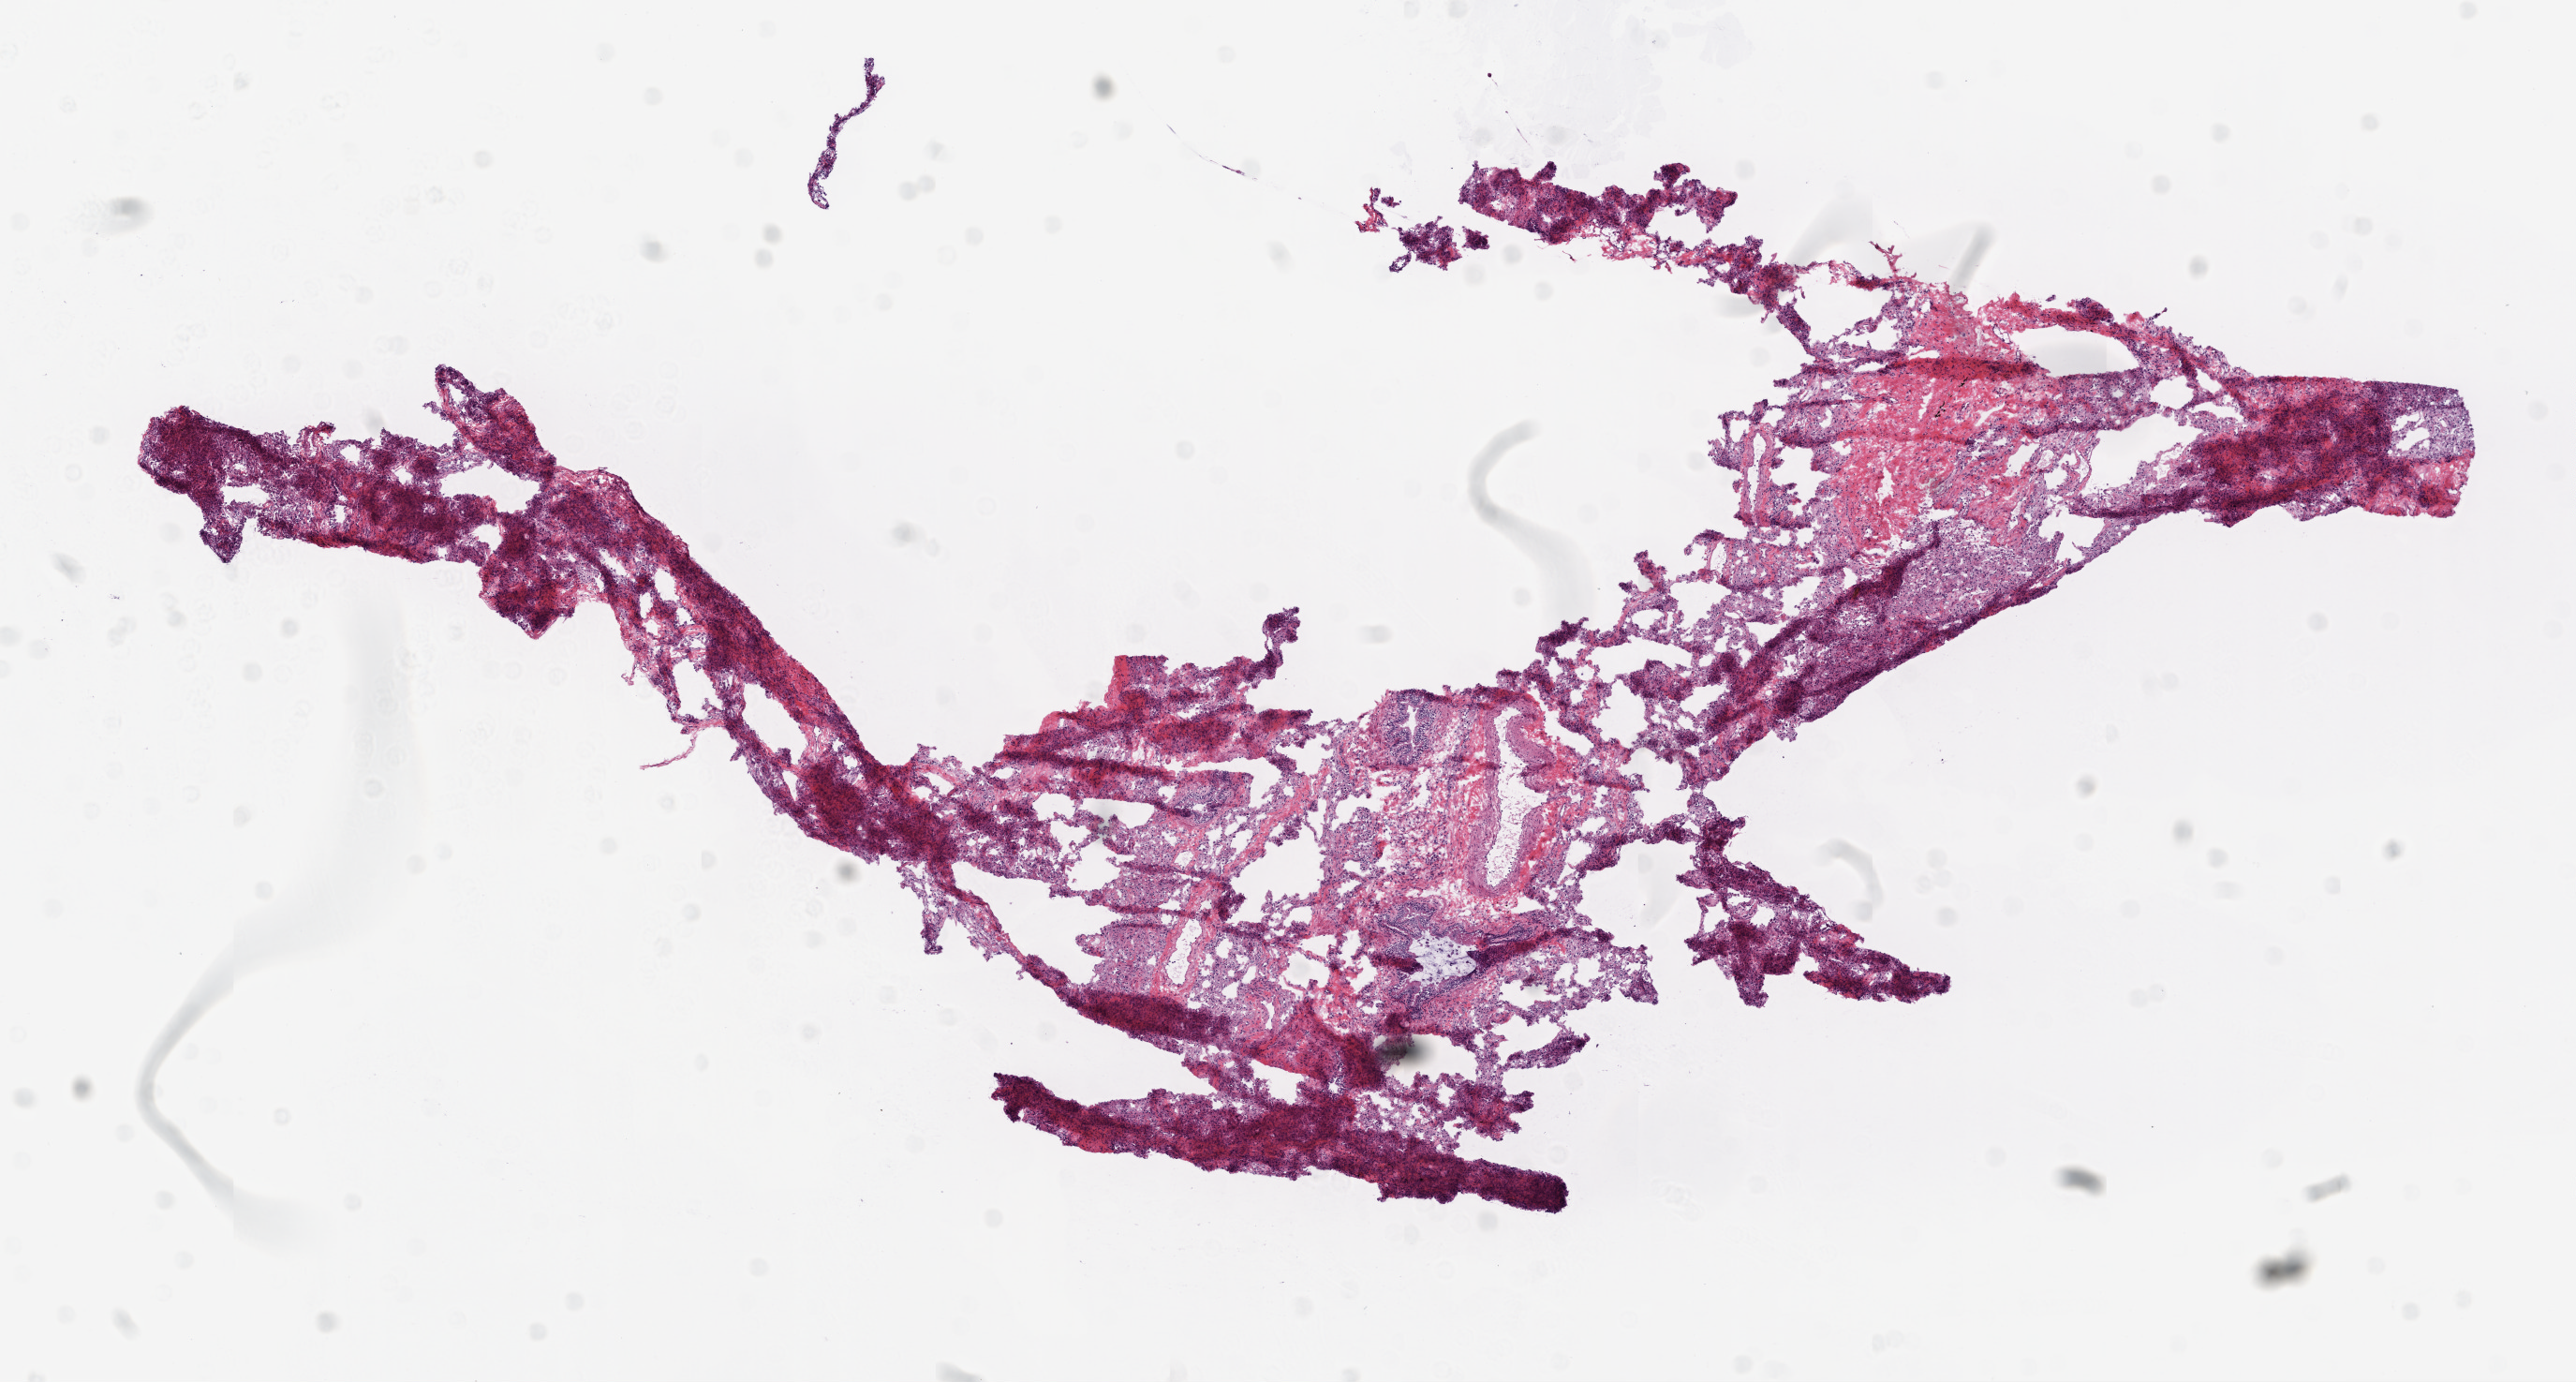
H&E whole-slide image — low-resolution overview of the scanned area, about 11.0 x 5.9 mm (slide scanned at 20x), frozen section, solid tissue normal (non-tumour tissue) sample from the lung. Female, age 63 years at initial diagnosis.
- this section: solid tissue normal (non-tumour) sample from the same patient
- patient diagnosis: Squamous cell carcinoma, NOS (upper lobe, lung)